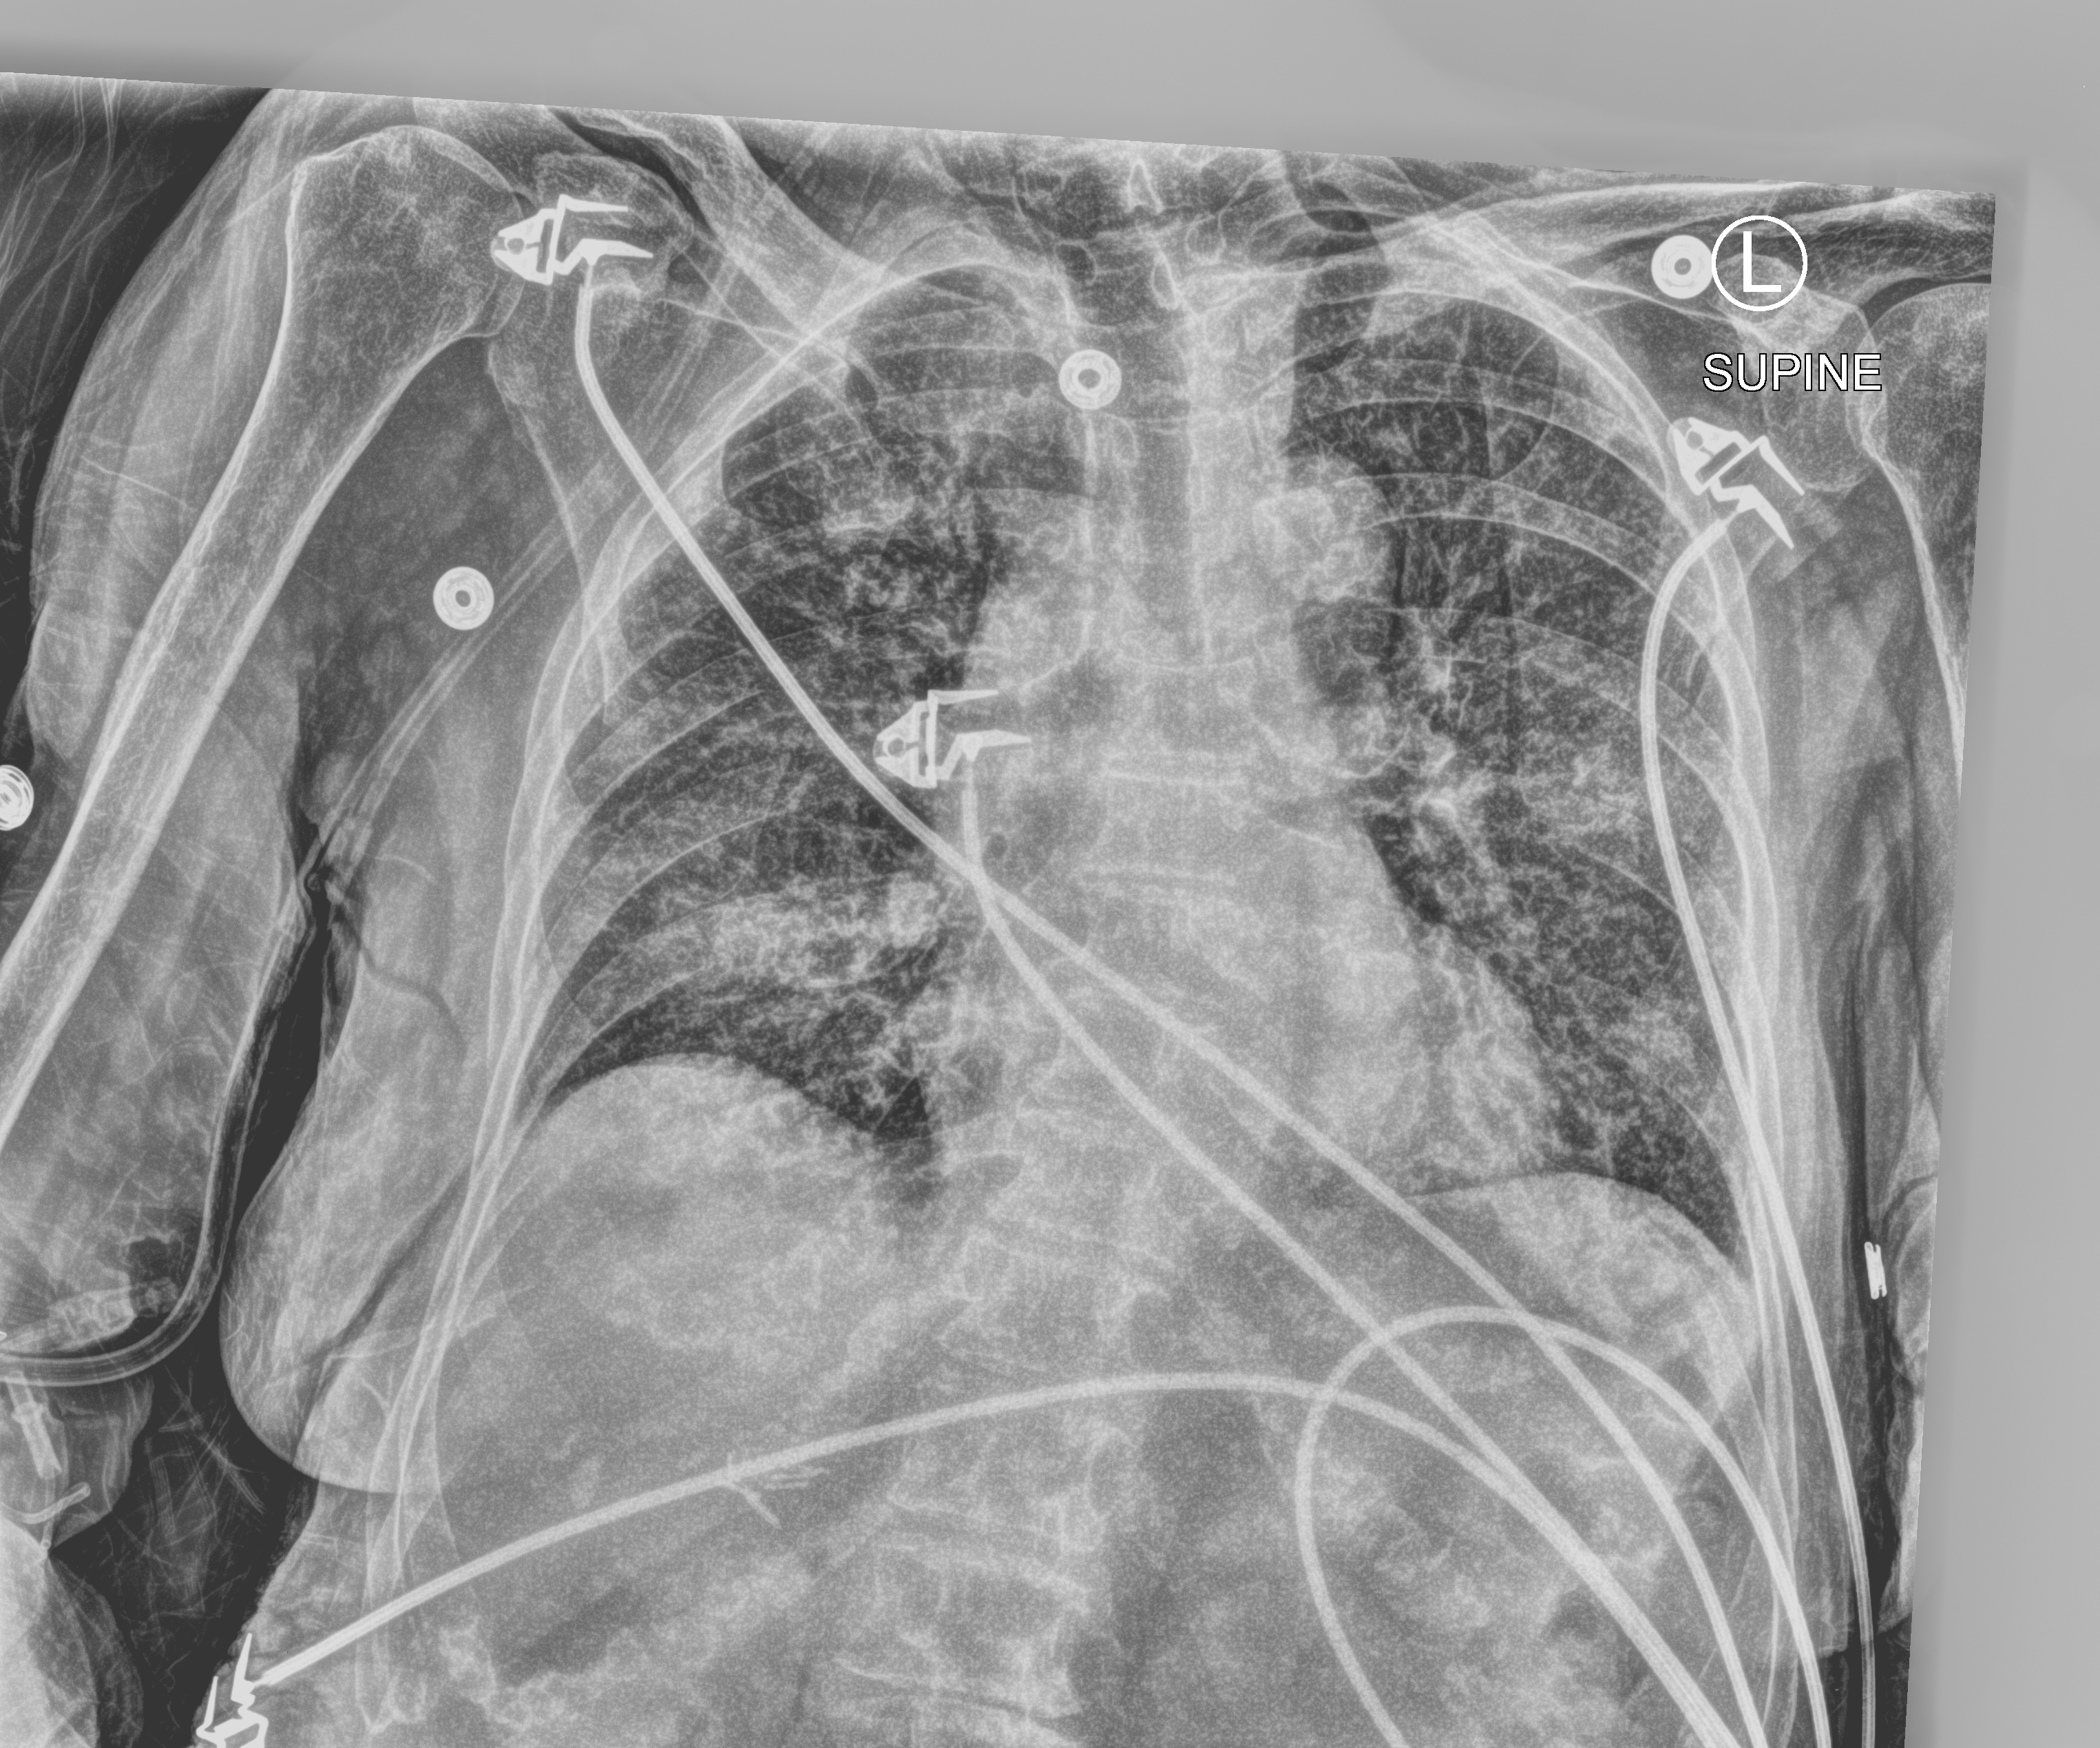
Bedside chest radiograph (computed radiography), anteroposterior (AP) projection. Patient hospitalised with COVID-19; female, aged 75–90 years.
Admission-level facts for this patient (not findings on this image; timing relative to this image not recorded):
- mechanically ventilated during this hospital stay: no
- hypertension (admission record): no
- admitted to intensive care during this hospital stay: no